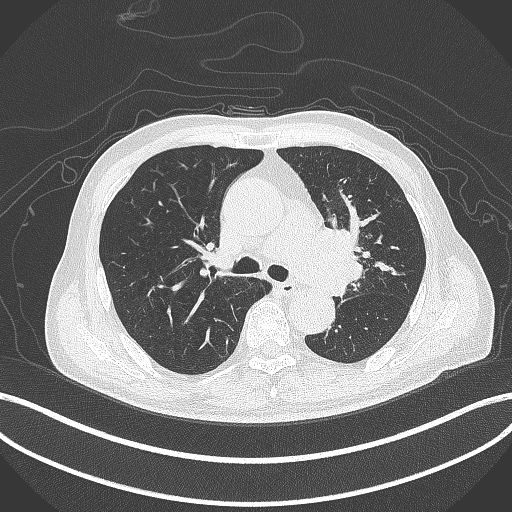
Chest CT, one axial slice; position 277 of 417 along the scan axis; 120 kVp; lung window (W 1500 / L -600 HU); 512 × 512 image matrix, field of view 400 × 400 mm. Patient: male, 77 years. Case-level facts recorded for this patient, not image findings: clinical TNM (as recorded): T3 N1 M0.
Structures marked on this image (bounding box drawn by a radiologist):
- lung tumour (recorded histology: adenocarcinoma): bounding box <314,216,369,303> (left, top, right, bottom; pixels)